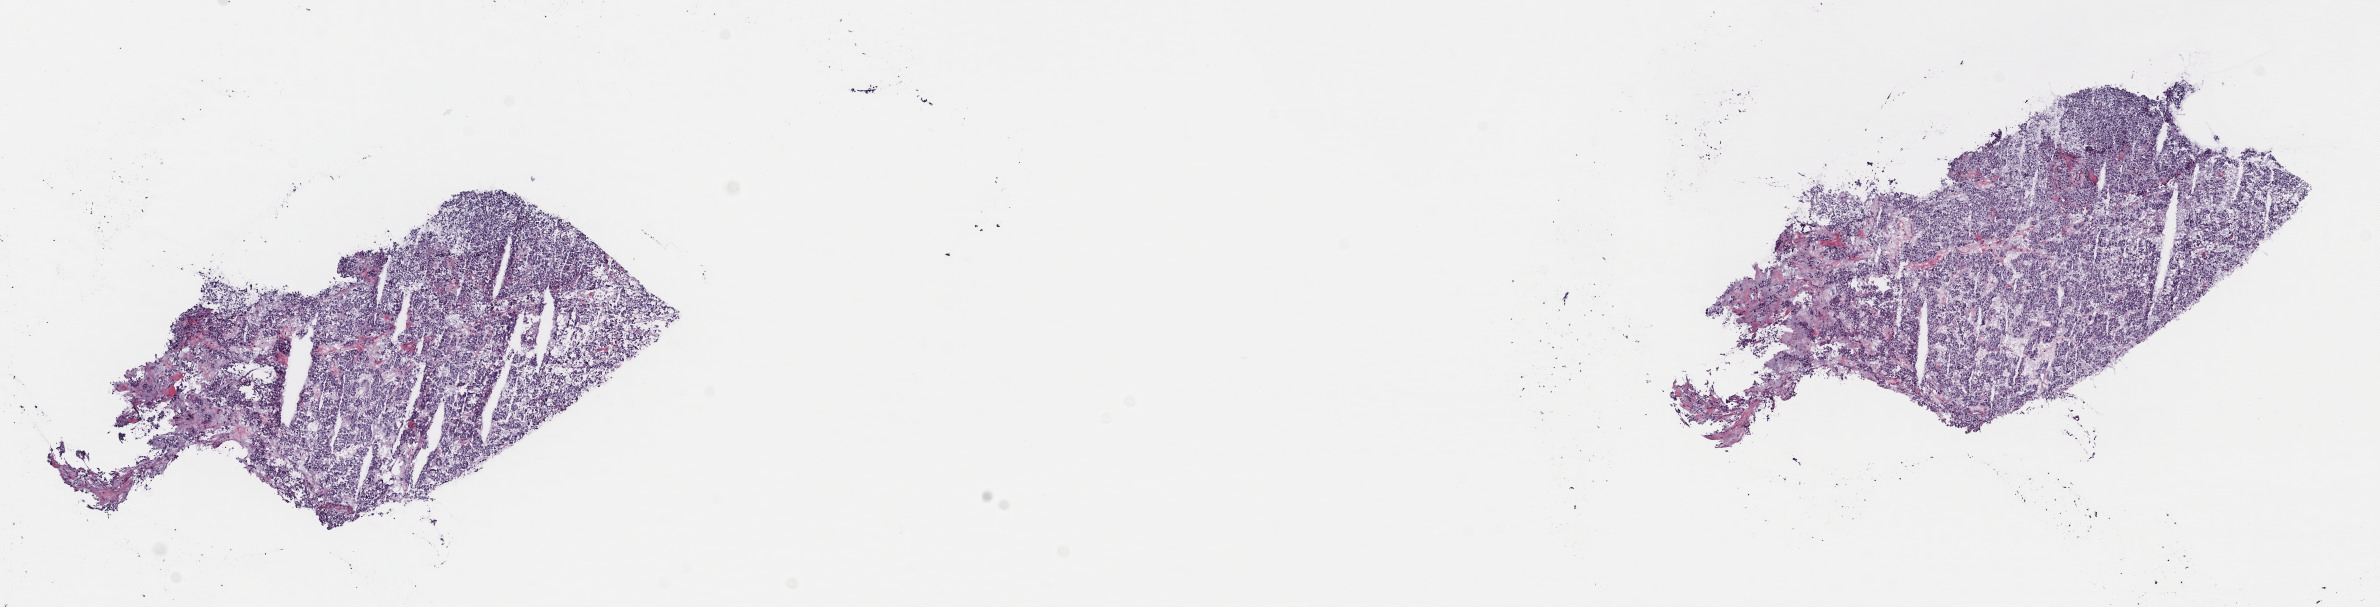
Hematoxylin and eosin (H&E) stained whole-slide image, a low-resolution overview of the entire scanned area, about 18.8 x 4.8 mm (from a 40x scan); frozen section; sample: primary tumour, adrenal gland. Female, age 51 years at initial diagnosis. Slide review estimates, as recorded: tumour cells 70%, tumour nuclei 100%, normal cells 0%, stromal cells 30%, necrosis 0%. Inflammatory infiltration, as recorded: lymphocyte infiltration 0%, monocyte infiltration 1%, neutrophil infiltration 0%.
Laterality: left. Histologic diagnosis: Pheochromocytoma, malignant.